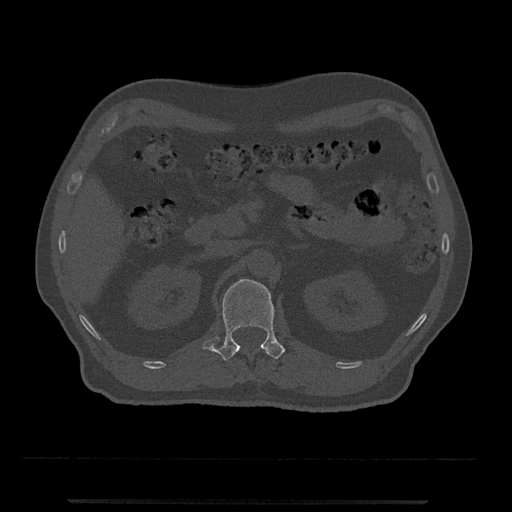
CT including the spine, one axial slice; position 348 of 797 along the scan axis; reconstruction kernel Br40s/3; bone window (W 1800 / L 400 HU); 0.5 mm slice thickness; 512 × 512 image matrix, field of view 419 × 419 mm. Patient: male, 63 years. From the clinical record (not read from this slice): primary cancer: prostate.
Structures marked on this image (semi-automatically segmented with operator editing):
- L1 vertebra: bounding box <202,279,286,361> (left, top, right, bottom; pixels)